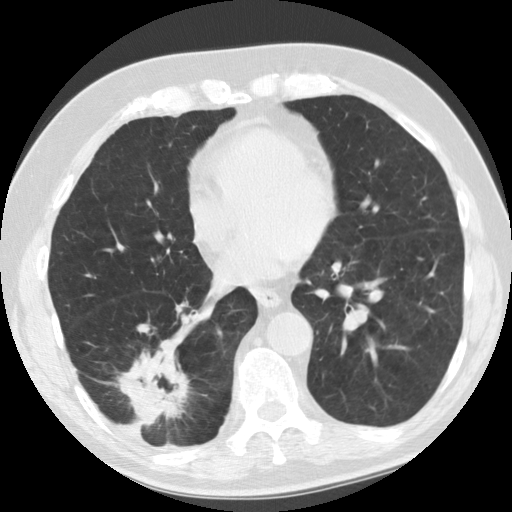
Low-dose screening chest CT, one axial slice; position 49 of 135 along the scan axis; lung window (W 1500 / L -600 HU); 512 × 512 image matrix, field of view 340 × 340 mm.
Outlined on this slice (manually delineated by an expert):
- lesion 1 (tumor, lower lobe of right lung): bounding box <116,344,190,427> (left, top, right, bottom; pixels)